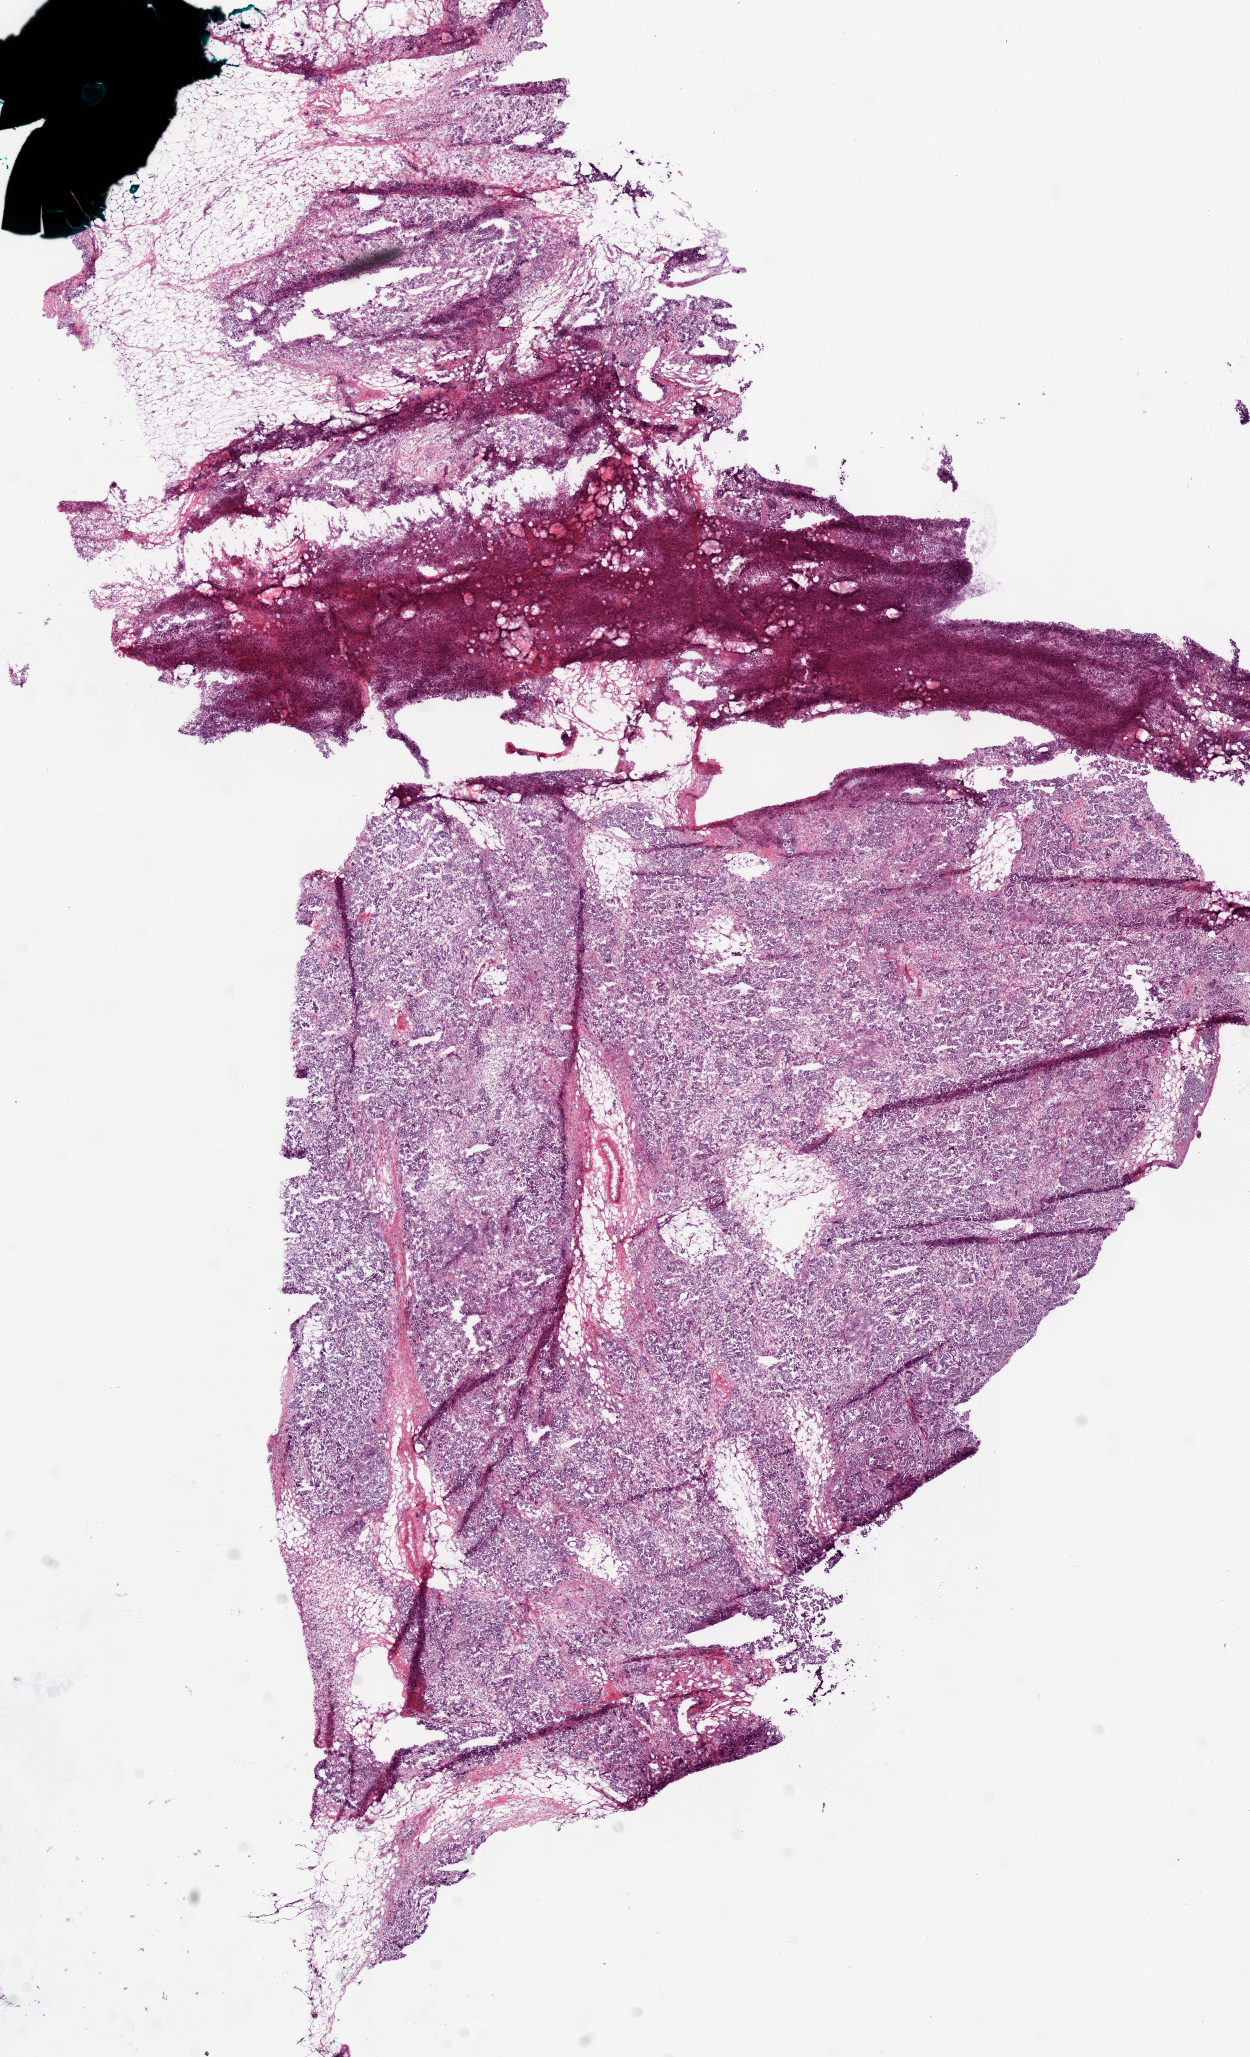
Whole-slide histology image, H&E — whole scanned area (about 10.0 x 16.5 mm, slide scanned at 20x) shown as a low-resolution overview; frozen section from the bottom of the tissue portion; sample: primary tumour, ovary. Female patient; age at initial diagnosis 58 years.
Pathologic diagnosis: Serous cystadenocarcinoma, NOS.